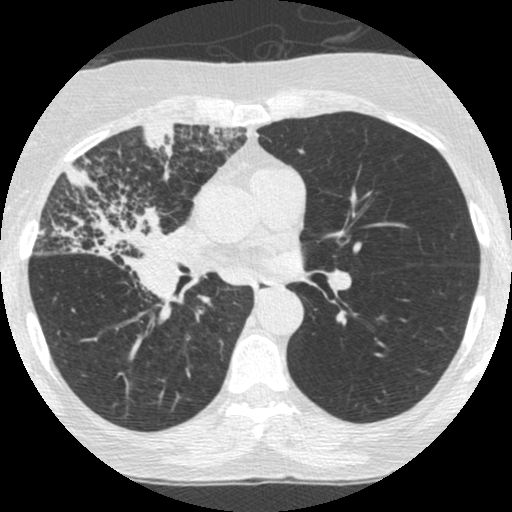
Low-dose screening chest CT, one axial slice. Slice 142 of 253 in the series (ordered by position). Reconstruction kernel STANDARD. 120 kVp. Lung window (W 1500 / L -600 HU). 1.25 mm slice thickness. 512 × 512 image matrix, field of view 294 × 294 mm.
Structures marked on this image (outlined manually by an expert reader):
- lesion 2 (tumor, hilum of right lung): bounding box <38,164,188,321> (left, top, right, bottom; pixels)
- lesion 3 (tumor, upper lobe of right lung): <142,122,175,182>
- lesion 4 (tumor, upper lobe of right lung): <207,125,242,152>